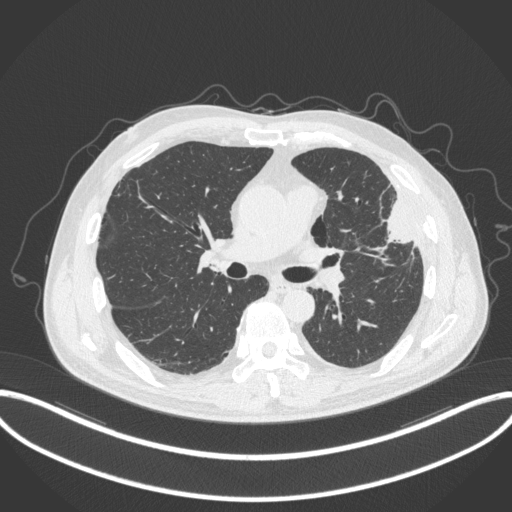
Chest CT, one axial slice; position 192 of 382 along the scan axis; reconstruction kernel B31f; lung window (W 1500 / L -600 HU); 1 mm slice thickness; 512 × 512 image matrix. Patient: male, 64 years. From the clinical record (not read from this slice): clinical TNM (as recorded): T4 N1 M0; histopathological grade: G3.
Outlined on this slice (bounding box drawn by a radiologist):
- lung tumour (recorded histology: adenocarcinoma): bounding box <376,195,414,247> (left, top, right, bottom; pixels)